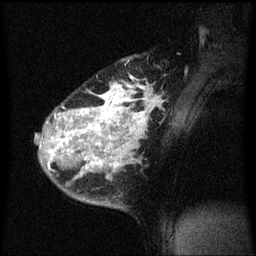
Breast MRI (dynamic contrast-enhanced), one sagittal slice. Dynamic contrast-enhanced series, image 2 of 3 at this slice position (ordered by acquisition). 1.5 T. TE 4.2 ms, TR 8.4 ms. 256 × 256 image matrix, field of view 200 × 200 mm. Patient: female, 34 years. Case-level facts recorded for this patient, not image findings: setting: breast cancer imaged before/during neoadjuvant chemotherapy; receptor status: HR-positive, HER2-negative.
Structures marked on this image (semi-automatically segmented with operator editing):
- analysis volume of interest (the breast-tissue region the enhancement analysis was run in; not a lesion): box from (x=36, y=54) to (x=159, y=209) px
- tumour enhancement mask (voxels above the 70 % enhancement threshold inside the analysis volume of interest): (x=48, y=76)–(x=157, y=173)